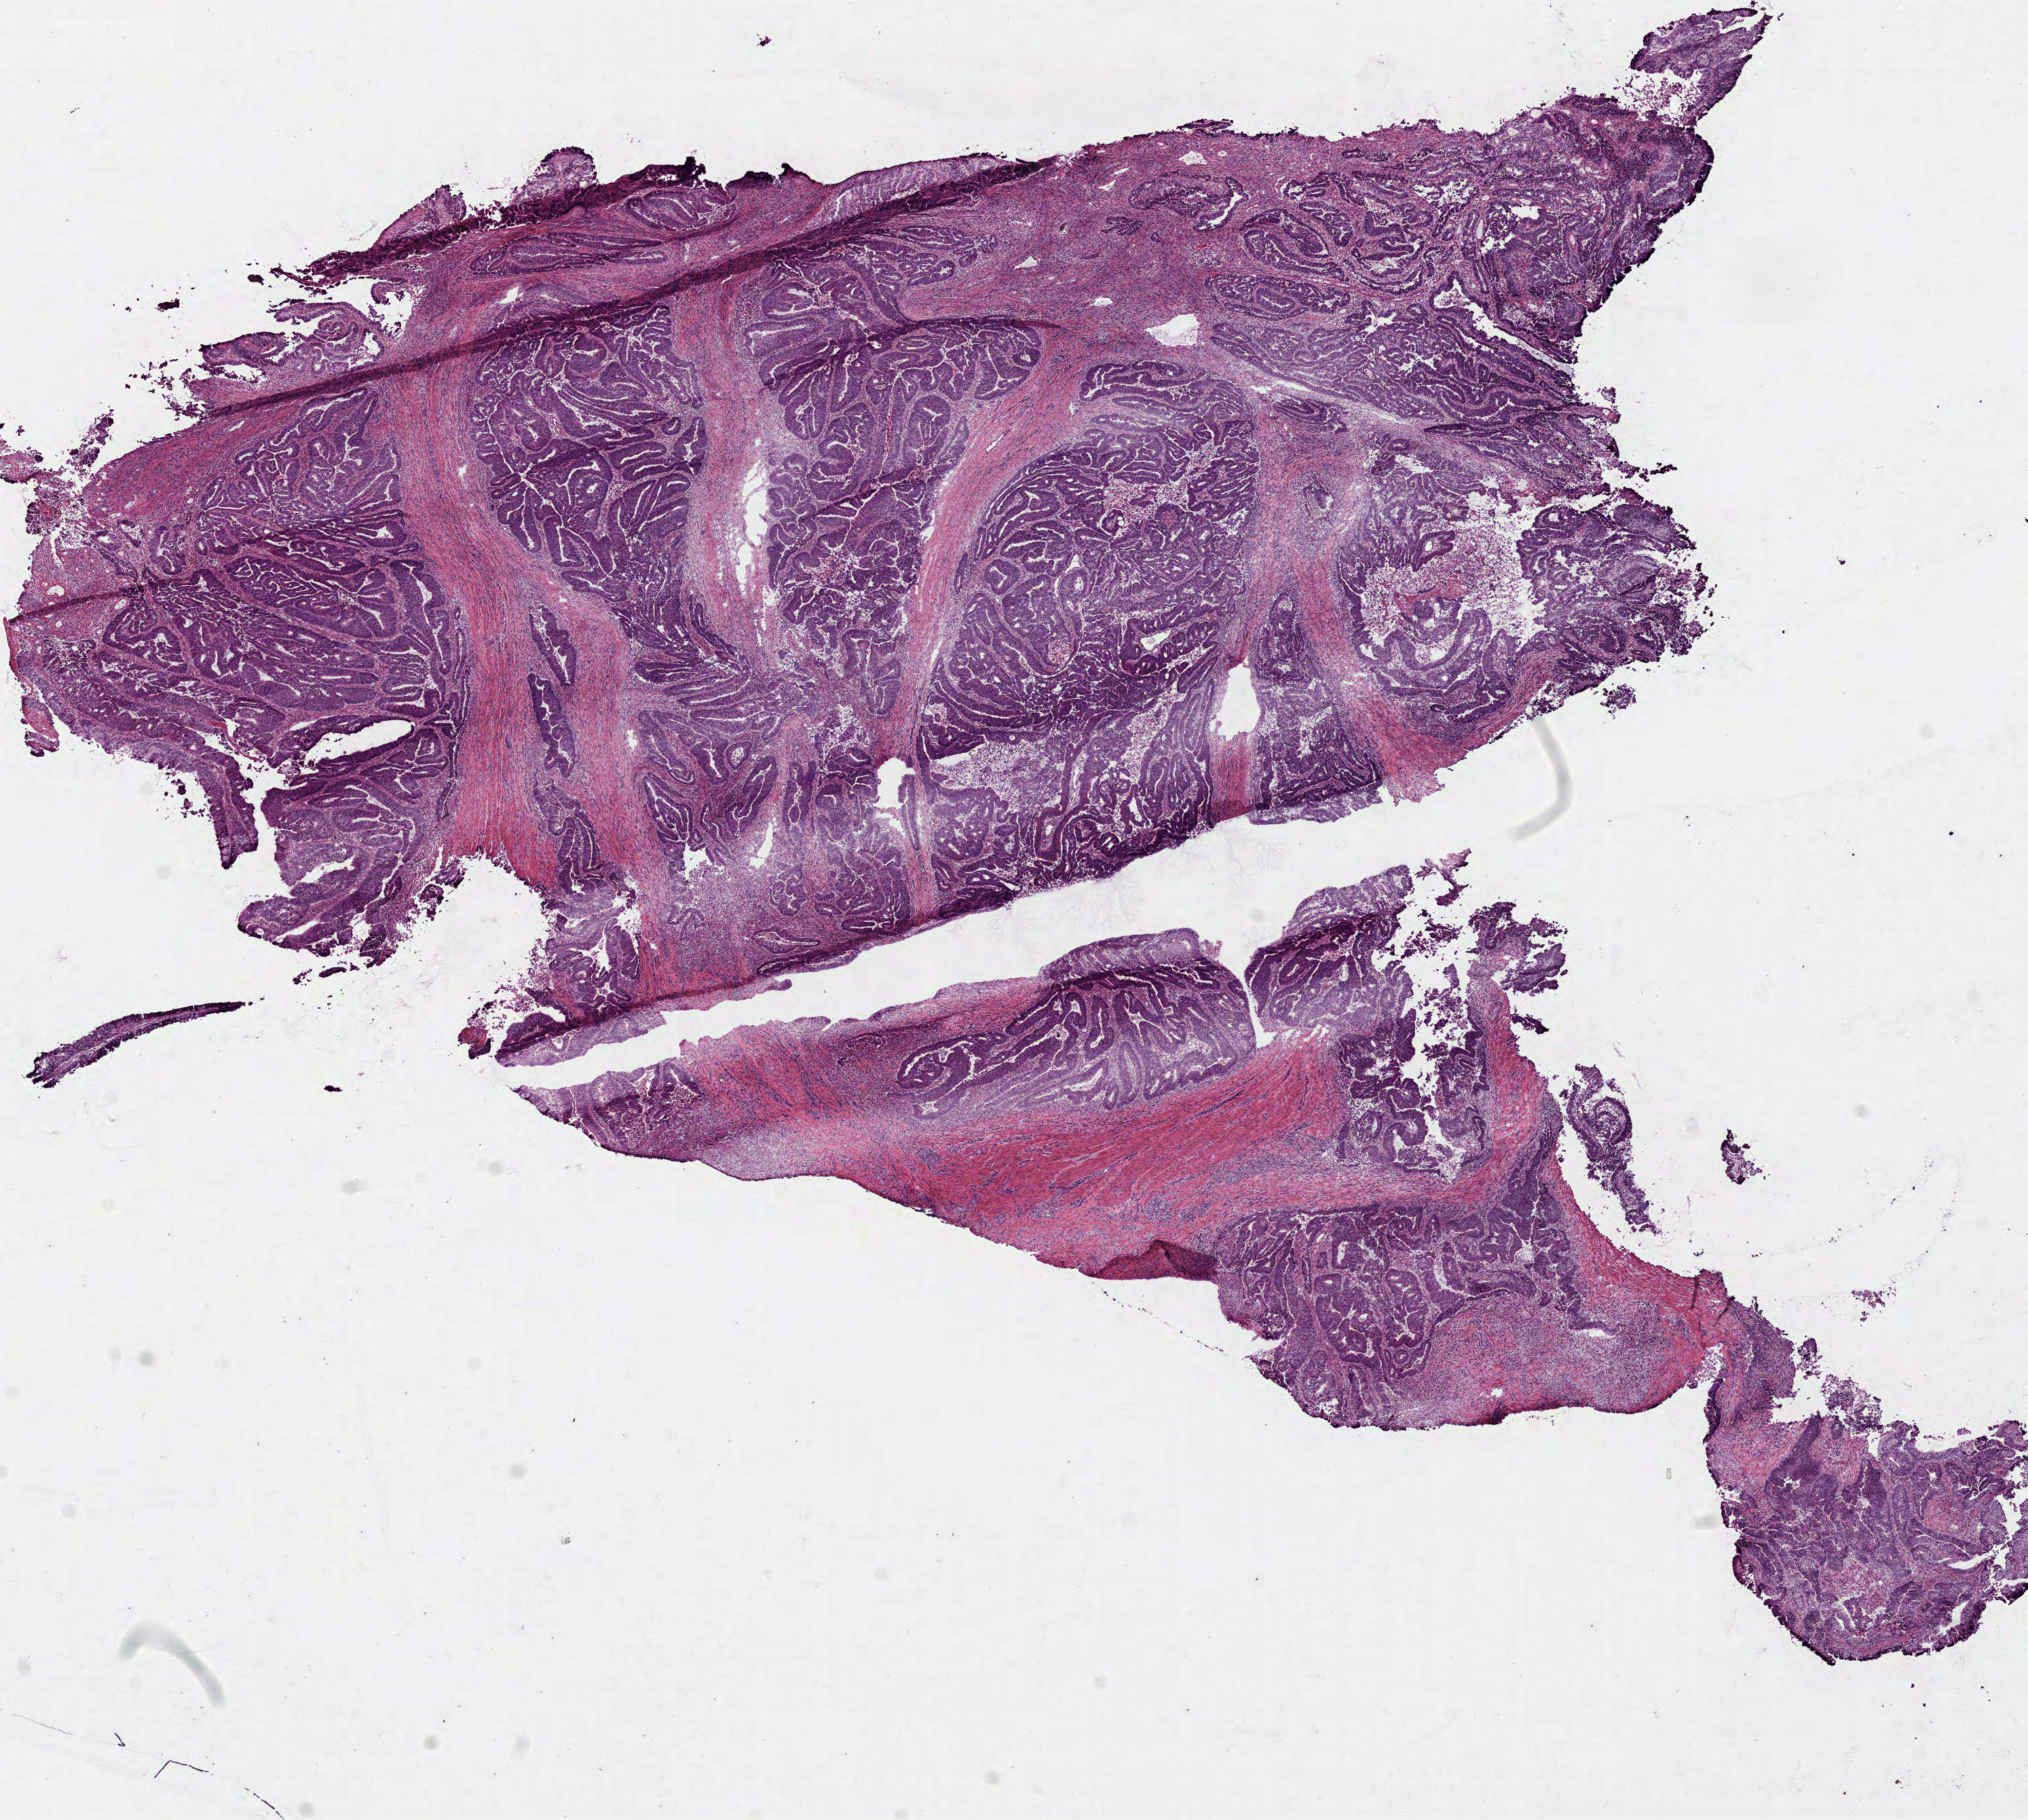
Whole-slide histology image, H&E-stained — whole scanned area (about 12.0 x 10.8 mm) shown as a low-resolution overview; frozen section from the bottom of the tissue portion; sample: primary tumour, rectum. Male patient; age at initial diagnosis 57 years. Slide review estimates, as recorded: tumour cells 67%, tumour nuclei 80%, normal cells 0%, stromal cells 25%, necrosis 8%.
• histologic diagnosis: Adenocarcinoma, NOS (rectosigmoid junction)
• AJCC pathologic stage: IIA